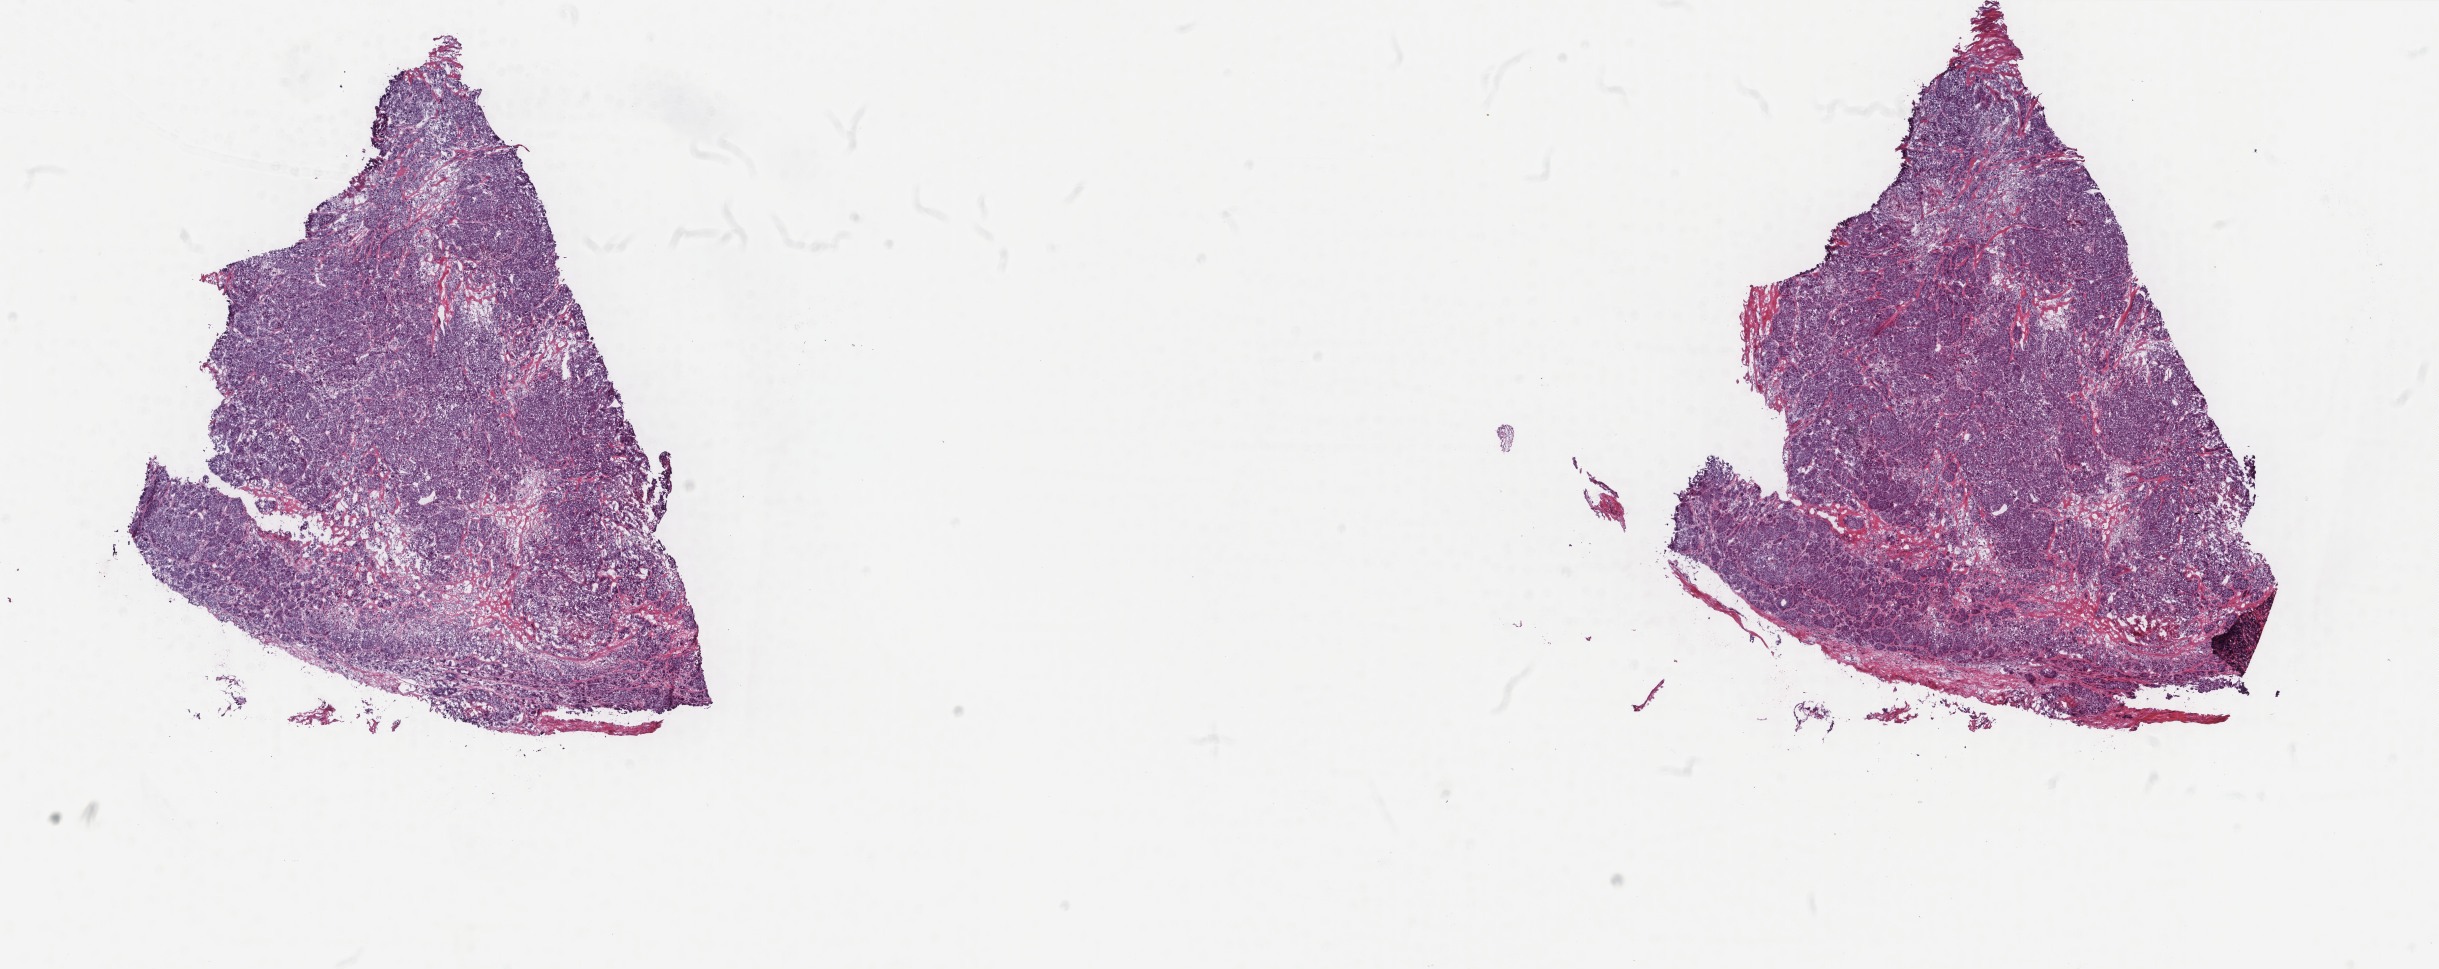
Whole-slide histology image, H&E, whole scanned area (about 19.4 x 7.7 mm, from a 40x scan) shown as a low-resolution overview; frozen section from the top of the tissue portion; metastatic tumour sample, sampled site: lymph nodes of axilla or arm. Male, age 77 years at initial diagnosis. Slide review estimates, as recorded: tumour cells 100%, tumour nuclei 95%, normal cells 0%, stromal cells 0%, necrosis 0%. Infiltration values recorded for this section: lymphocyte infiltration 0%, monocyte infiltration 0%, neutrophil infiltration 0%.
- this section: metastatic tumour tissue
- patient diagnosis: Malignant melanoma, NOS